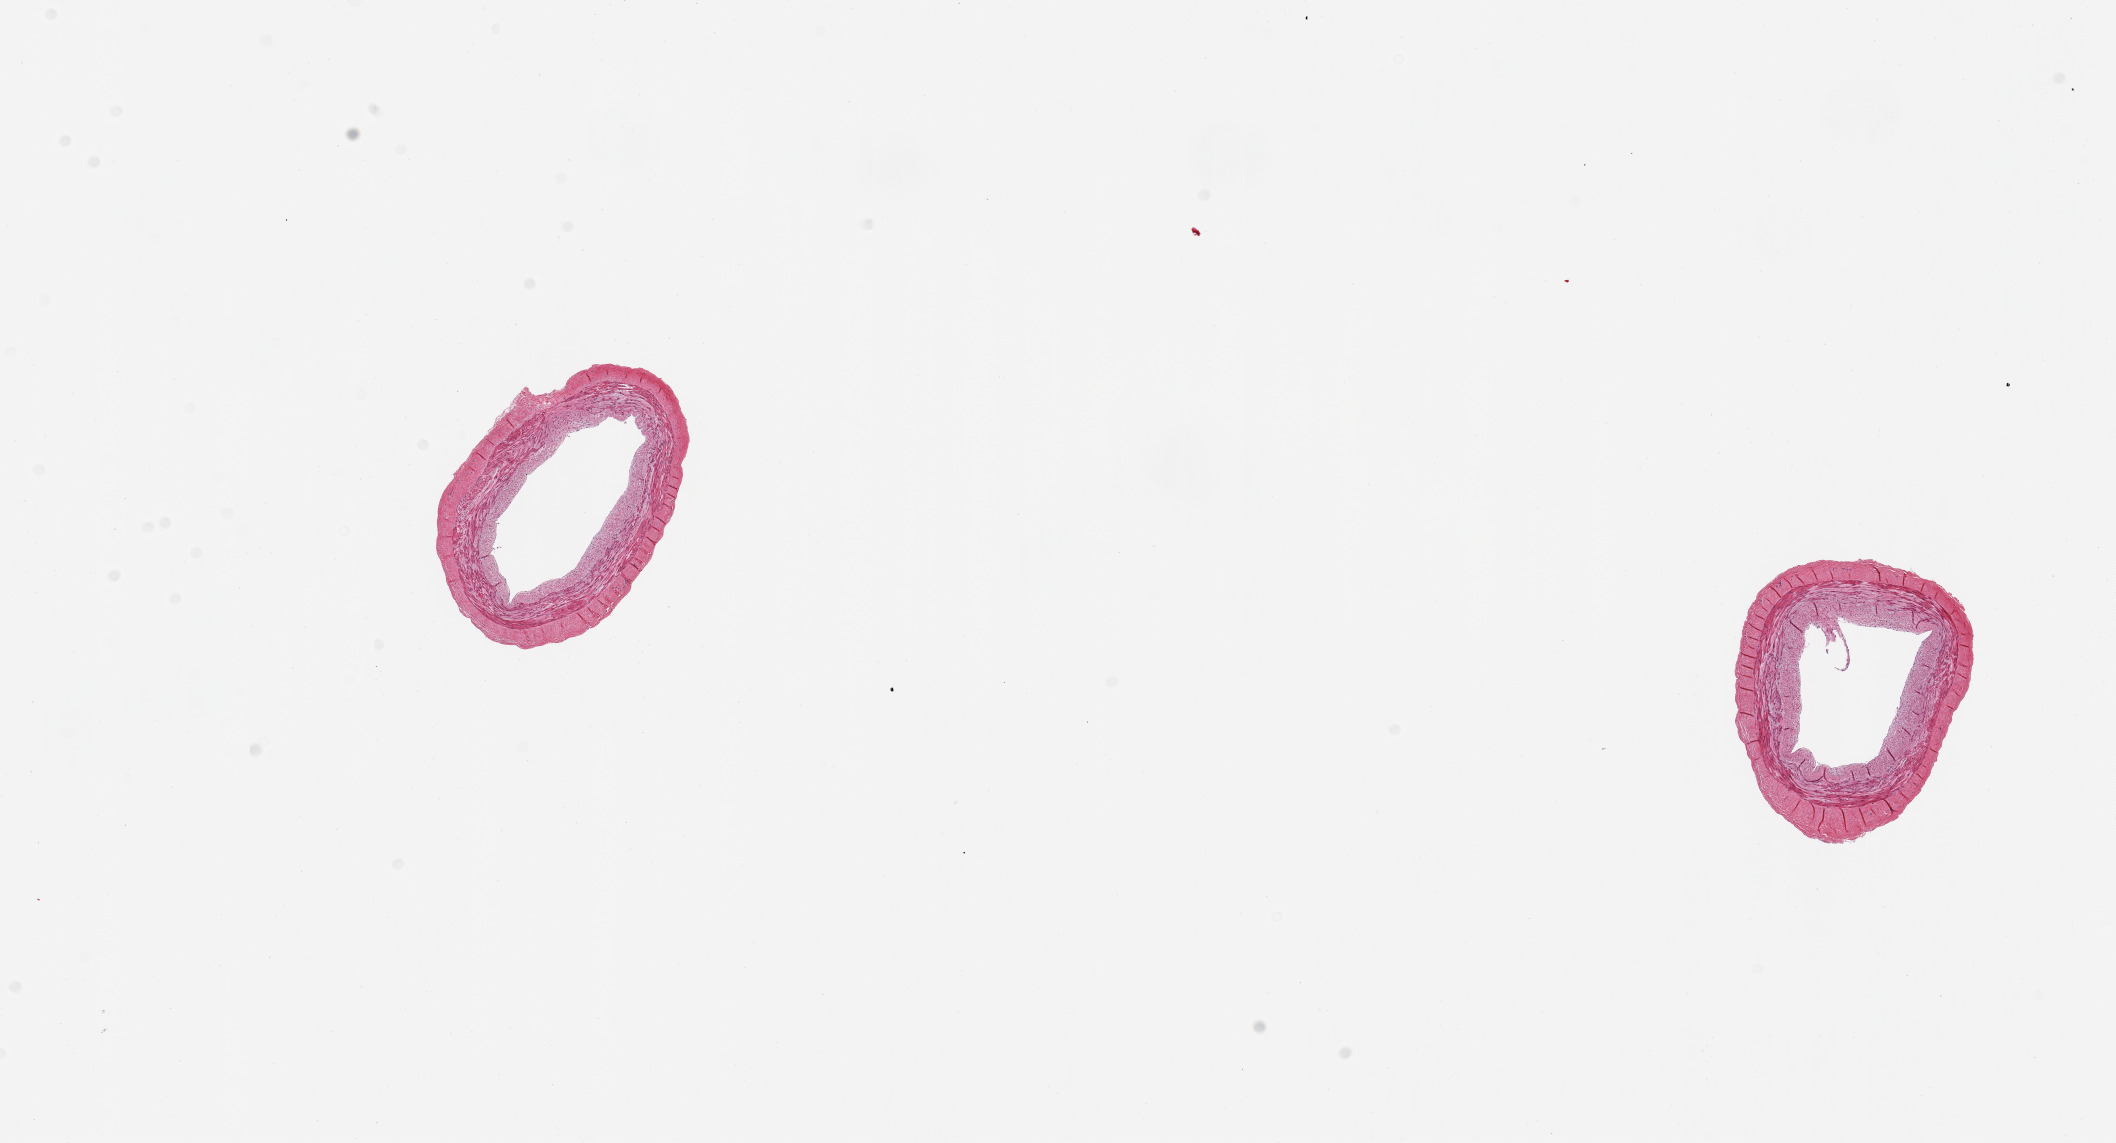
Hematoxylin and eosin (H&E) whole-slide image, low-resolution overview of the scanned area, about 16.7 x 9.0 mm, PAXgene-fixed paraffin-embedded (PFPE) section, section of tibial artery (target tissue), donor tissue sample. Female donor.
Pathologist's review note for this sample: 2 pieces, no atherosis, no adherent fat, clean specimens.